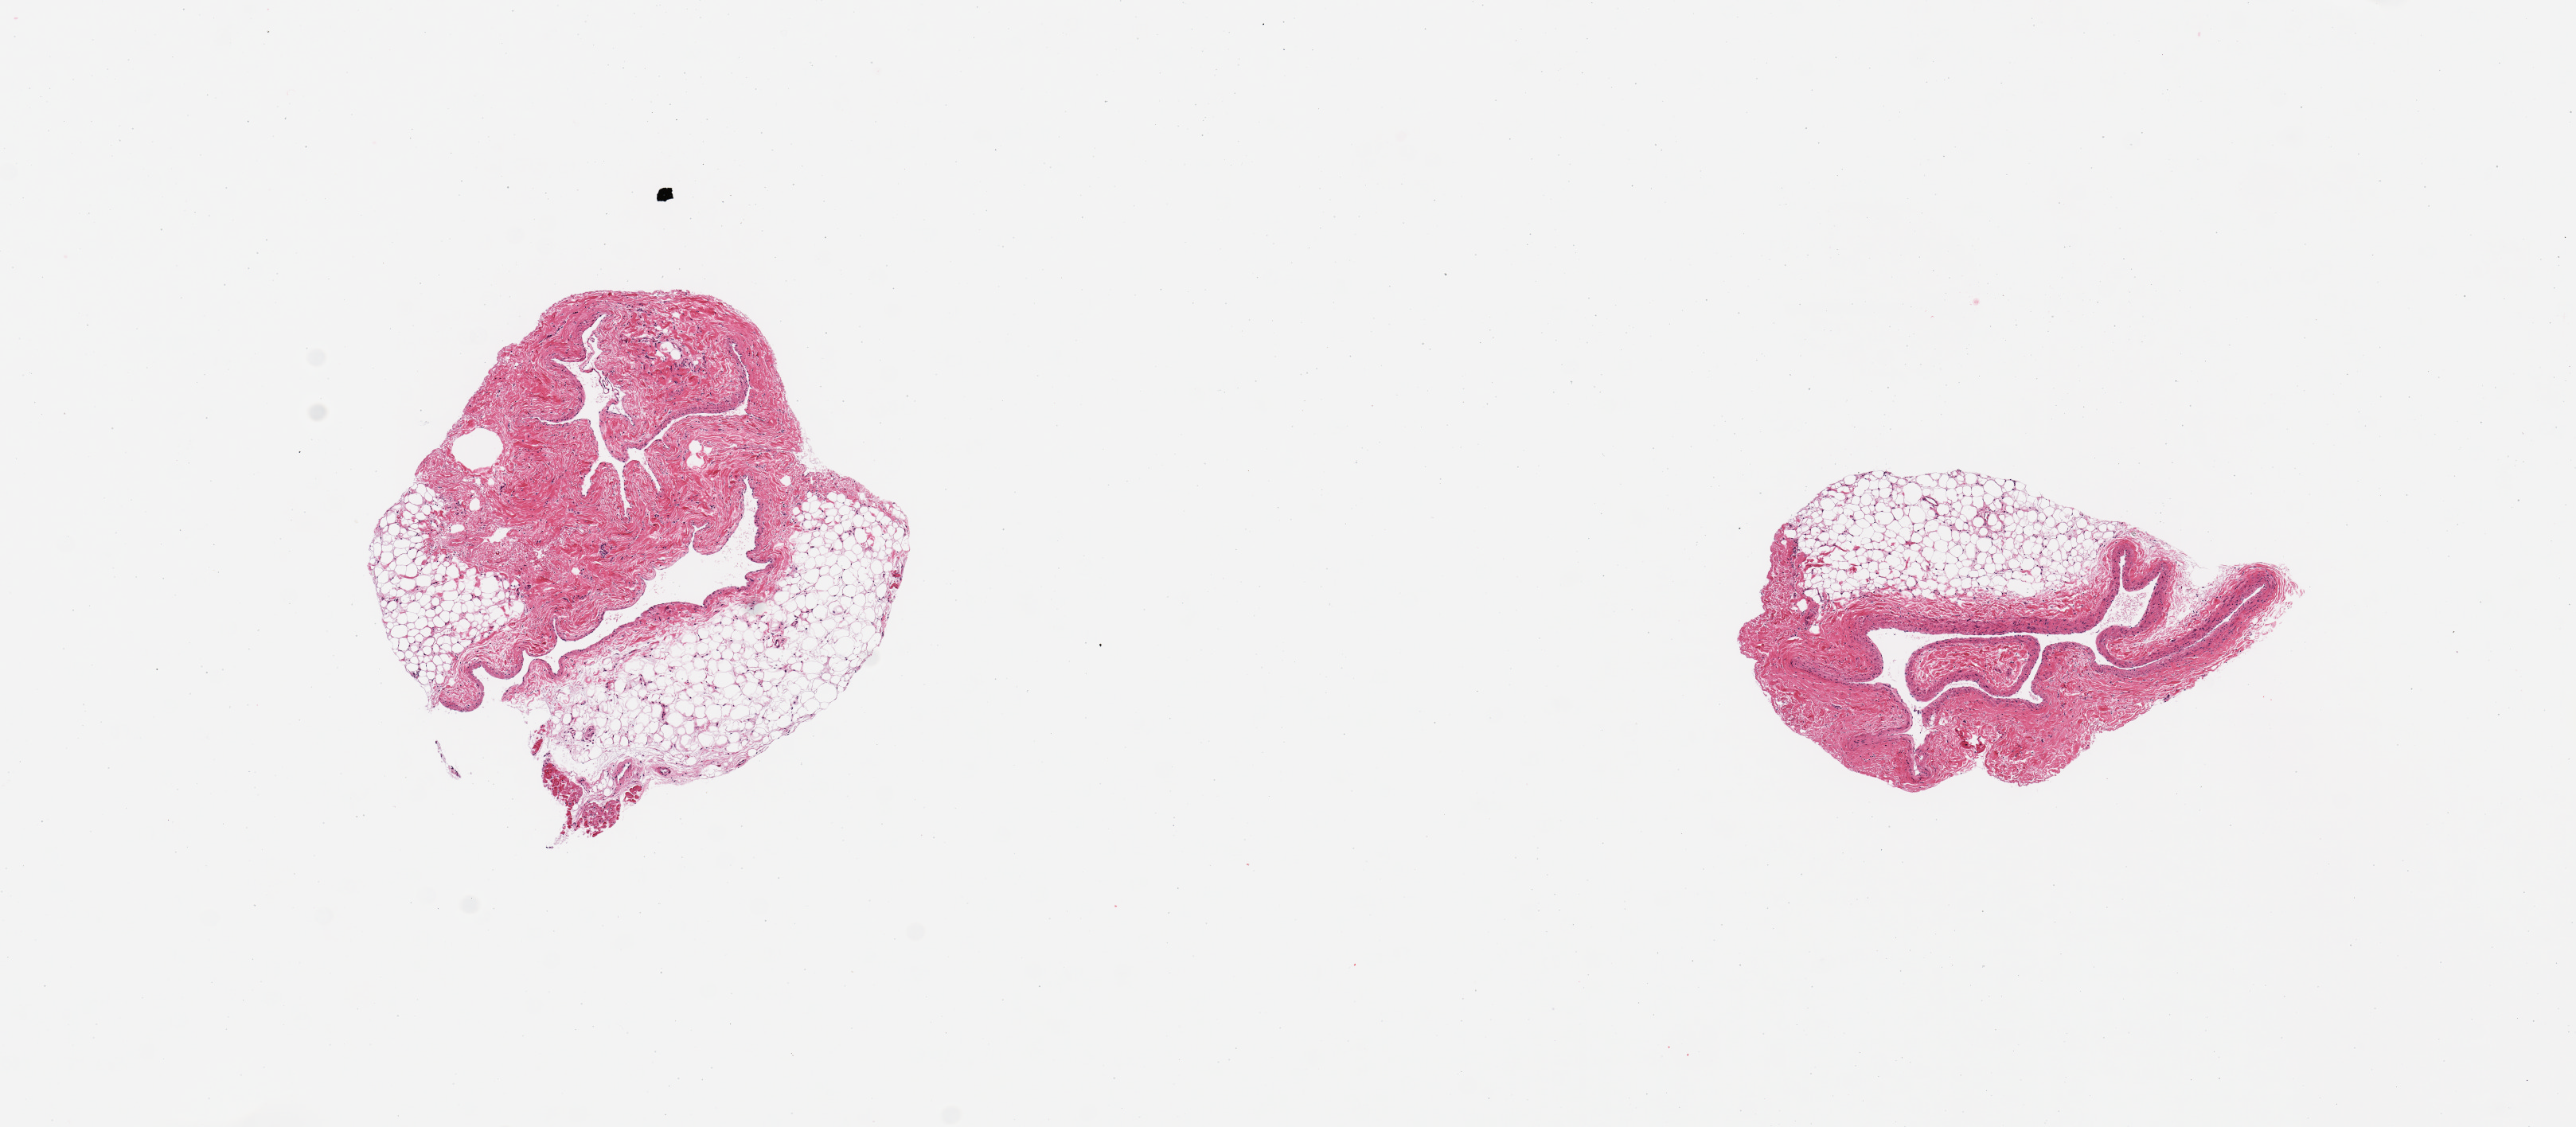
Digitized hematoxylin and eosin (H&E)-stained section — whole scanned area (about 12.8 x 5.6 mm) shown as a low-resolution overview; PAXgene-fixed, paraffin-embedded tissue; target tissue: coronary artery; donor tissue sample. Donor sex: female.
Reviewer comment on this tissue sample: 2 pieces, not coronary artery, venous sinus and epicardial fat/myocardium.